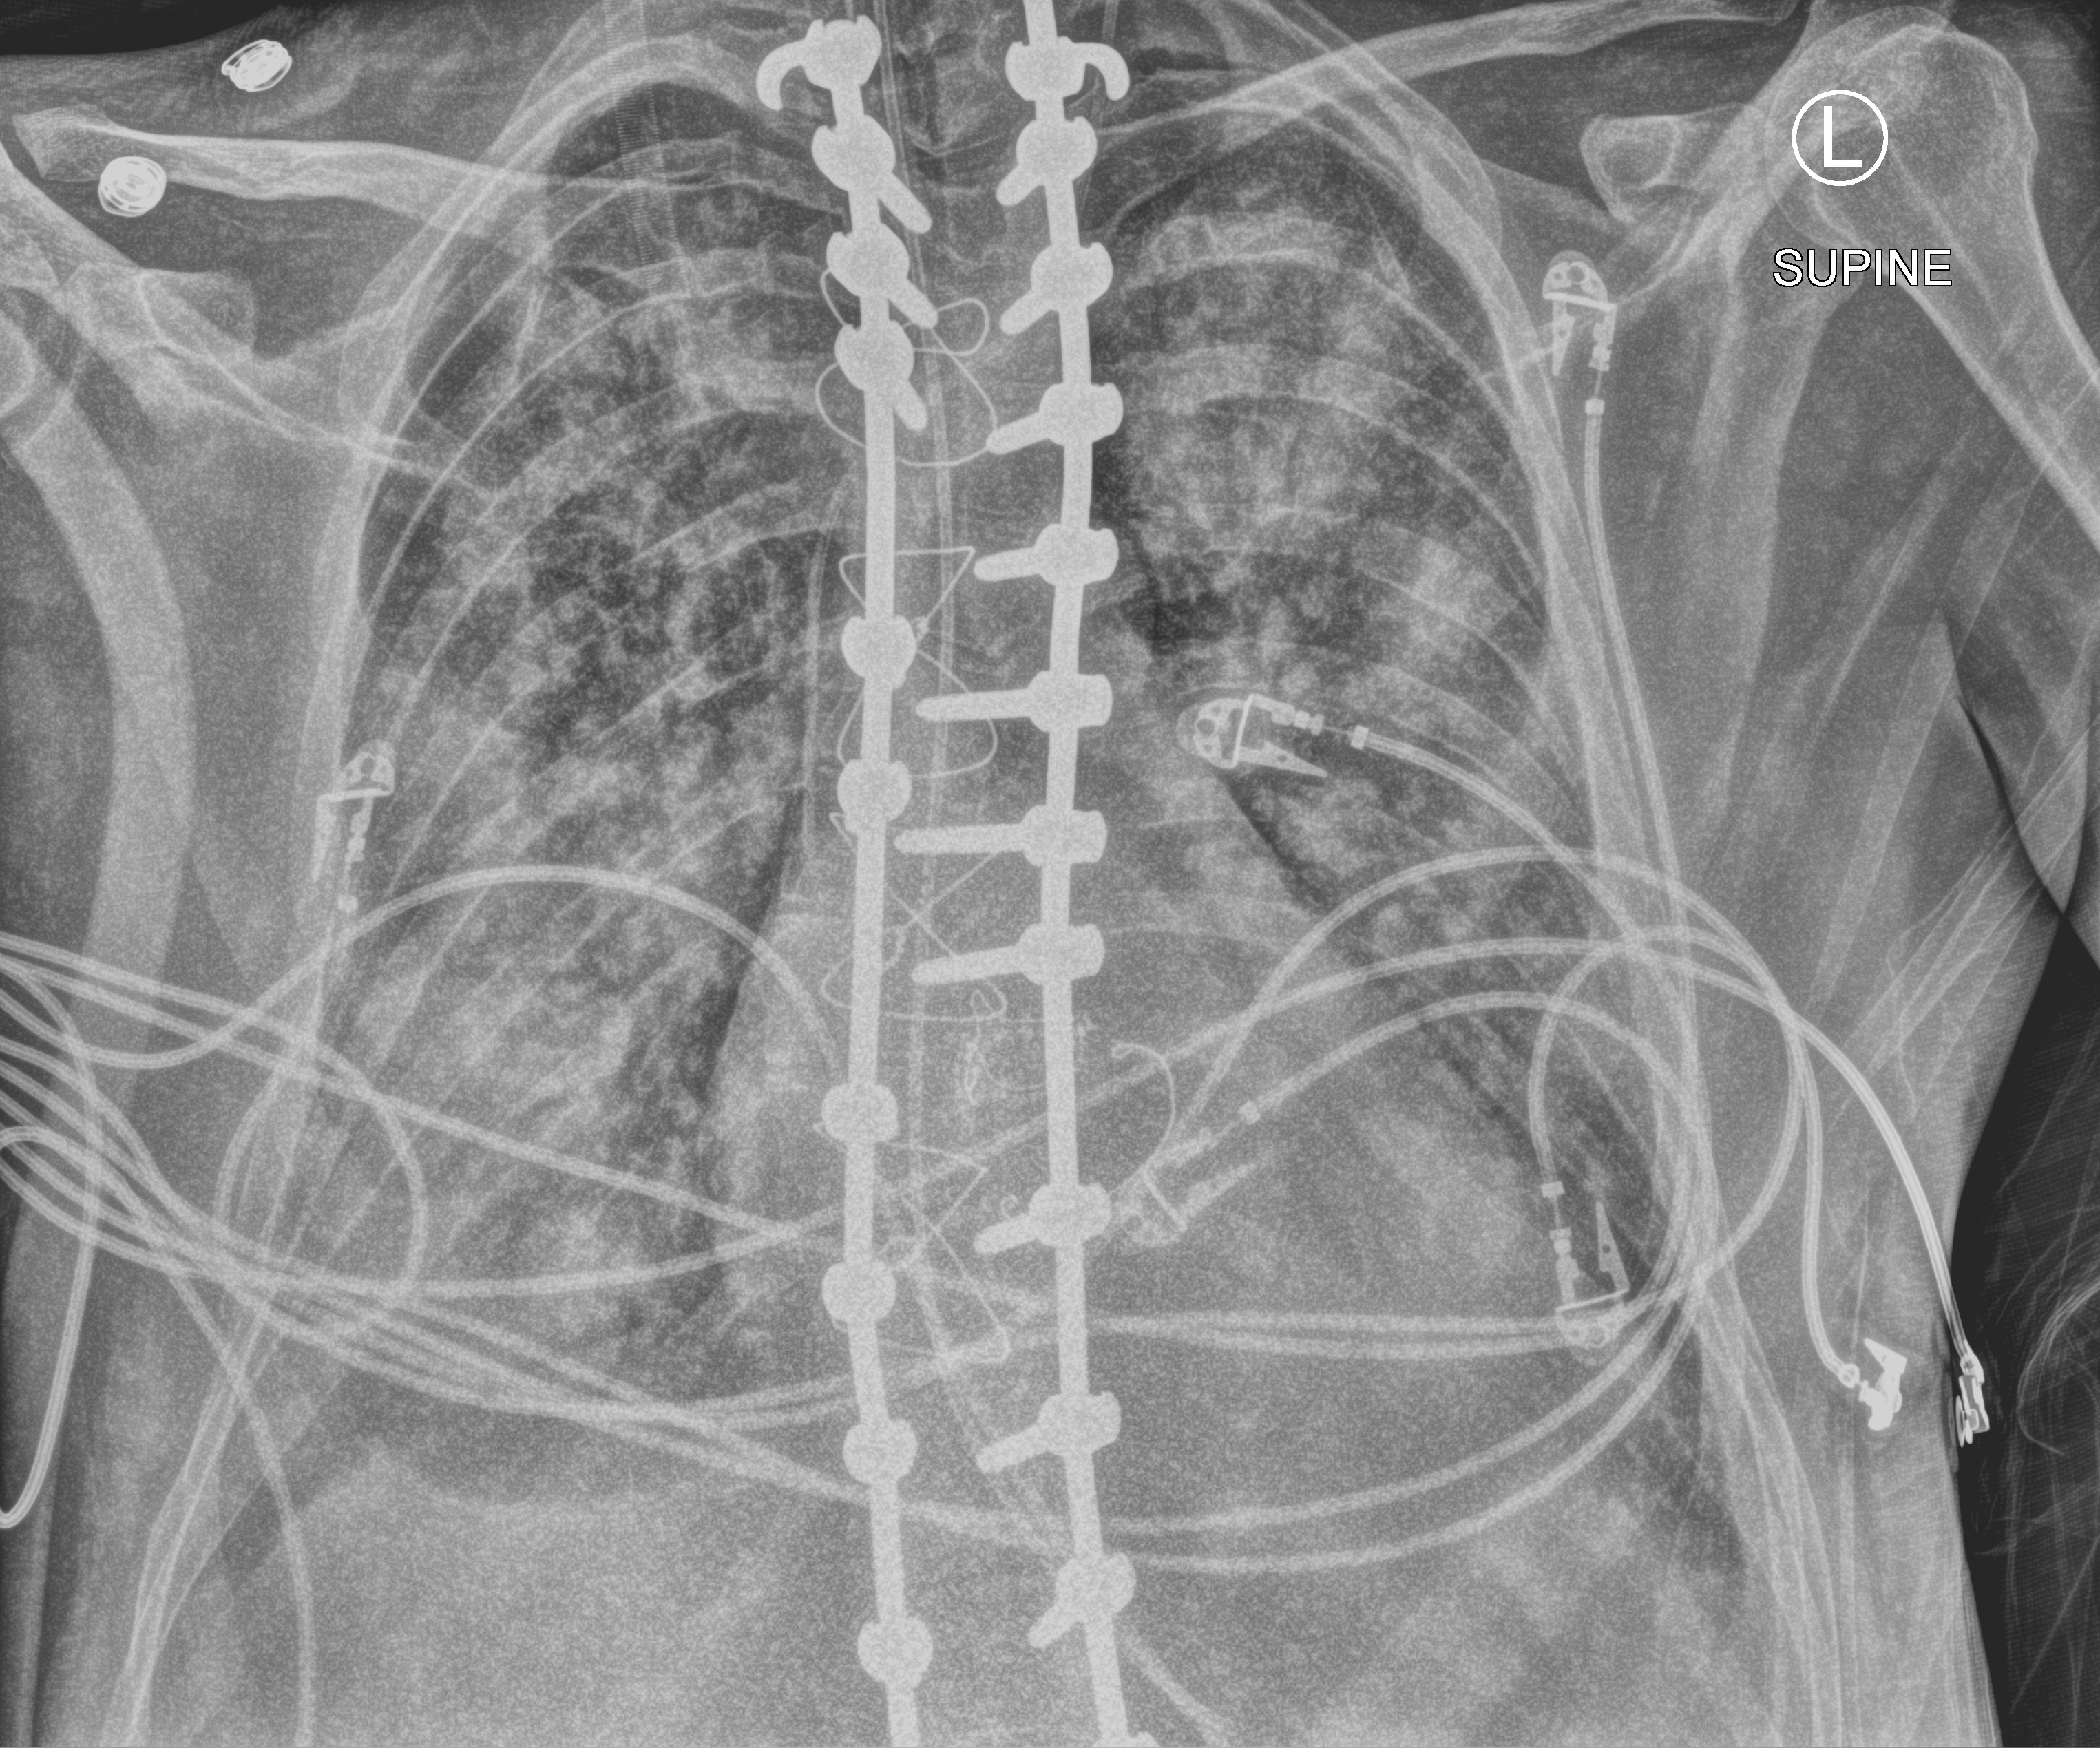
Bedside chest radiograph (computed radiography); anteroposterior (AP) projection. Adult patient hospitalised with COVID-19, age 18–59 years.
Hospital-stay facts (about this admission, not read from this image; timing relative to this image not recorded):
- mechanically ventilated during this hospital stay: yes
- admitted to intensive care during this hospital stay: yes